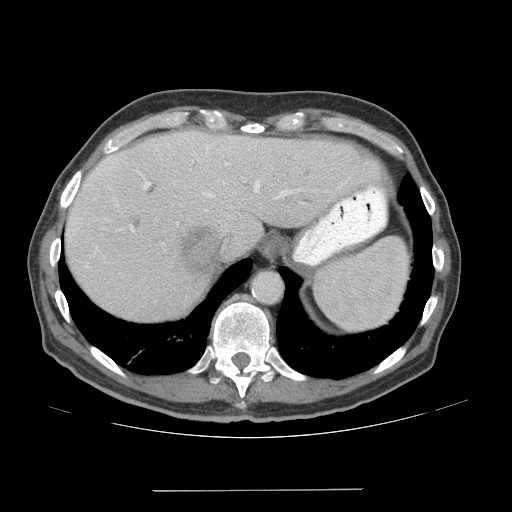
Contrast-enhanced abdominal CT (liver protocol), one axial slice; position 54 of 77 along the scan axis; soft-tissue window (W 400 / L 40 HU); 2.5 mm slice thickness; 512 × 512 image matrix, field of view 400 × 400 mm. Case-level facts recorded for this patient, not image findings: diagnosis: hepatocellular carcinoma (patient treated with transarterial chemoembolisation; whether this scan precedes or follows treatment is not stated here); TNM stage (as recorded): Stage-IVA; Child-Pugh class: A; tumour differentiation: well differentiated; tumour nodularity: uninodular.
Outlined on this slice (semi-automatic segmentation, software-assisted and operator-edited):
- liver parenchyma outside the tumour (the mass and vessels are separate outlines, so this box may not span the whole liver): box from (x=64, y=130) to (x=380, y=320) px
- mass: (x=174, y=226)–(x=225, y=276)
- liver vessels: (x=96, y=144)–(x=304, y=250)